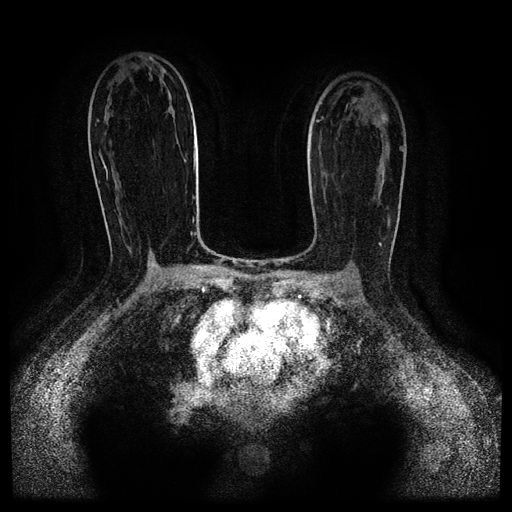
Breast MRI (dynamic contrast-enhanced, multi-phase), one axial slice; slice 60 of 116 in the series (ordered by position); dynamic contrast-enhanced series, time point 2 of 5 at this slice position (early post-contrast); 1.5 T; TE 2.6 ms, TR 5.3 ms; 2 mm slice thickness; 512 × 512 image matrix, field of view 350 × 350 mm. Female patient, age 52 years.
Outlined on this slice (semi-automatically segmented with operator editing):
- breast lesion (labelled 'tumour' in the annotation; benign lesions carry a separate 'benign' label): box from (x=382, y=116) to (x=386, y=120) px